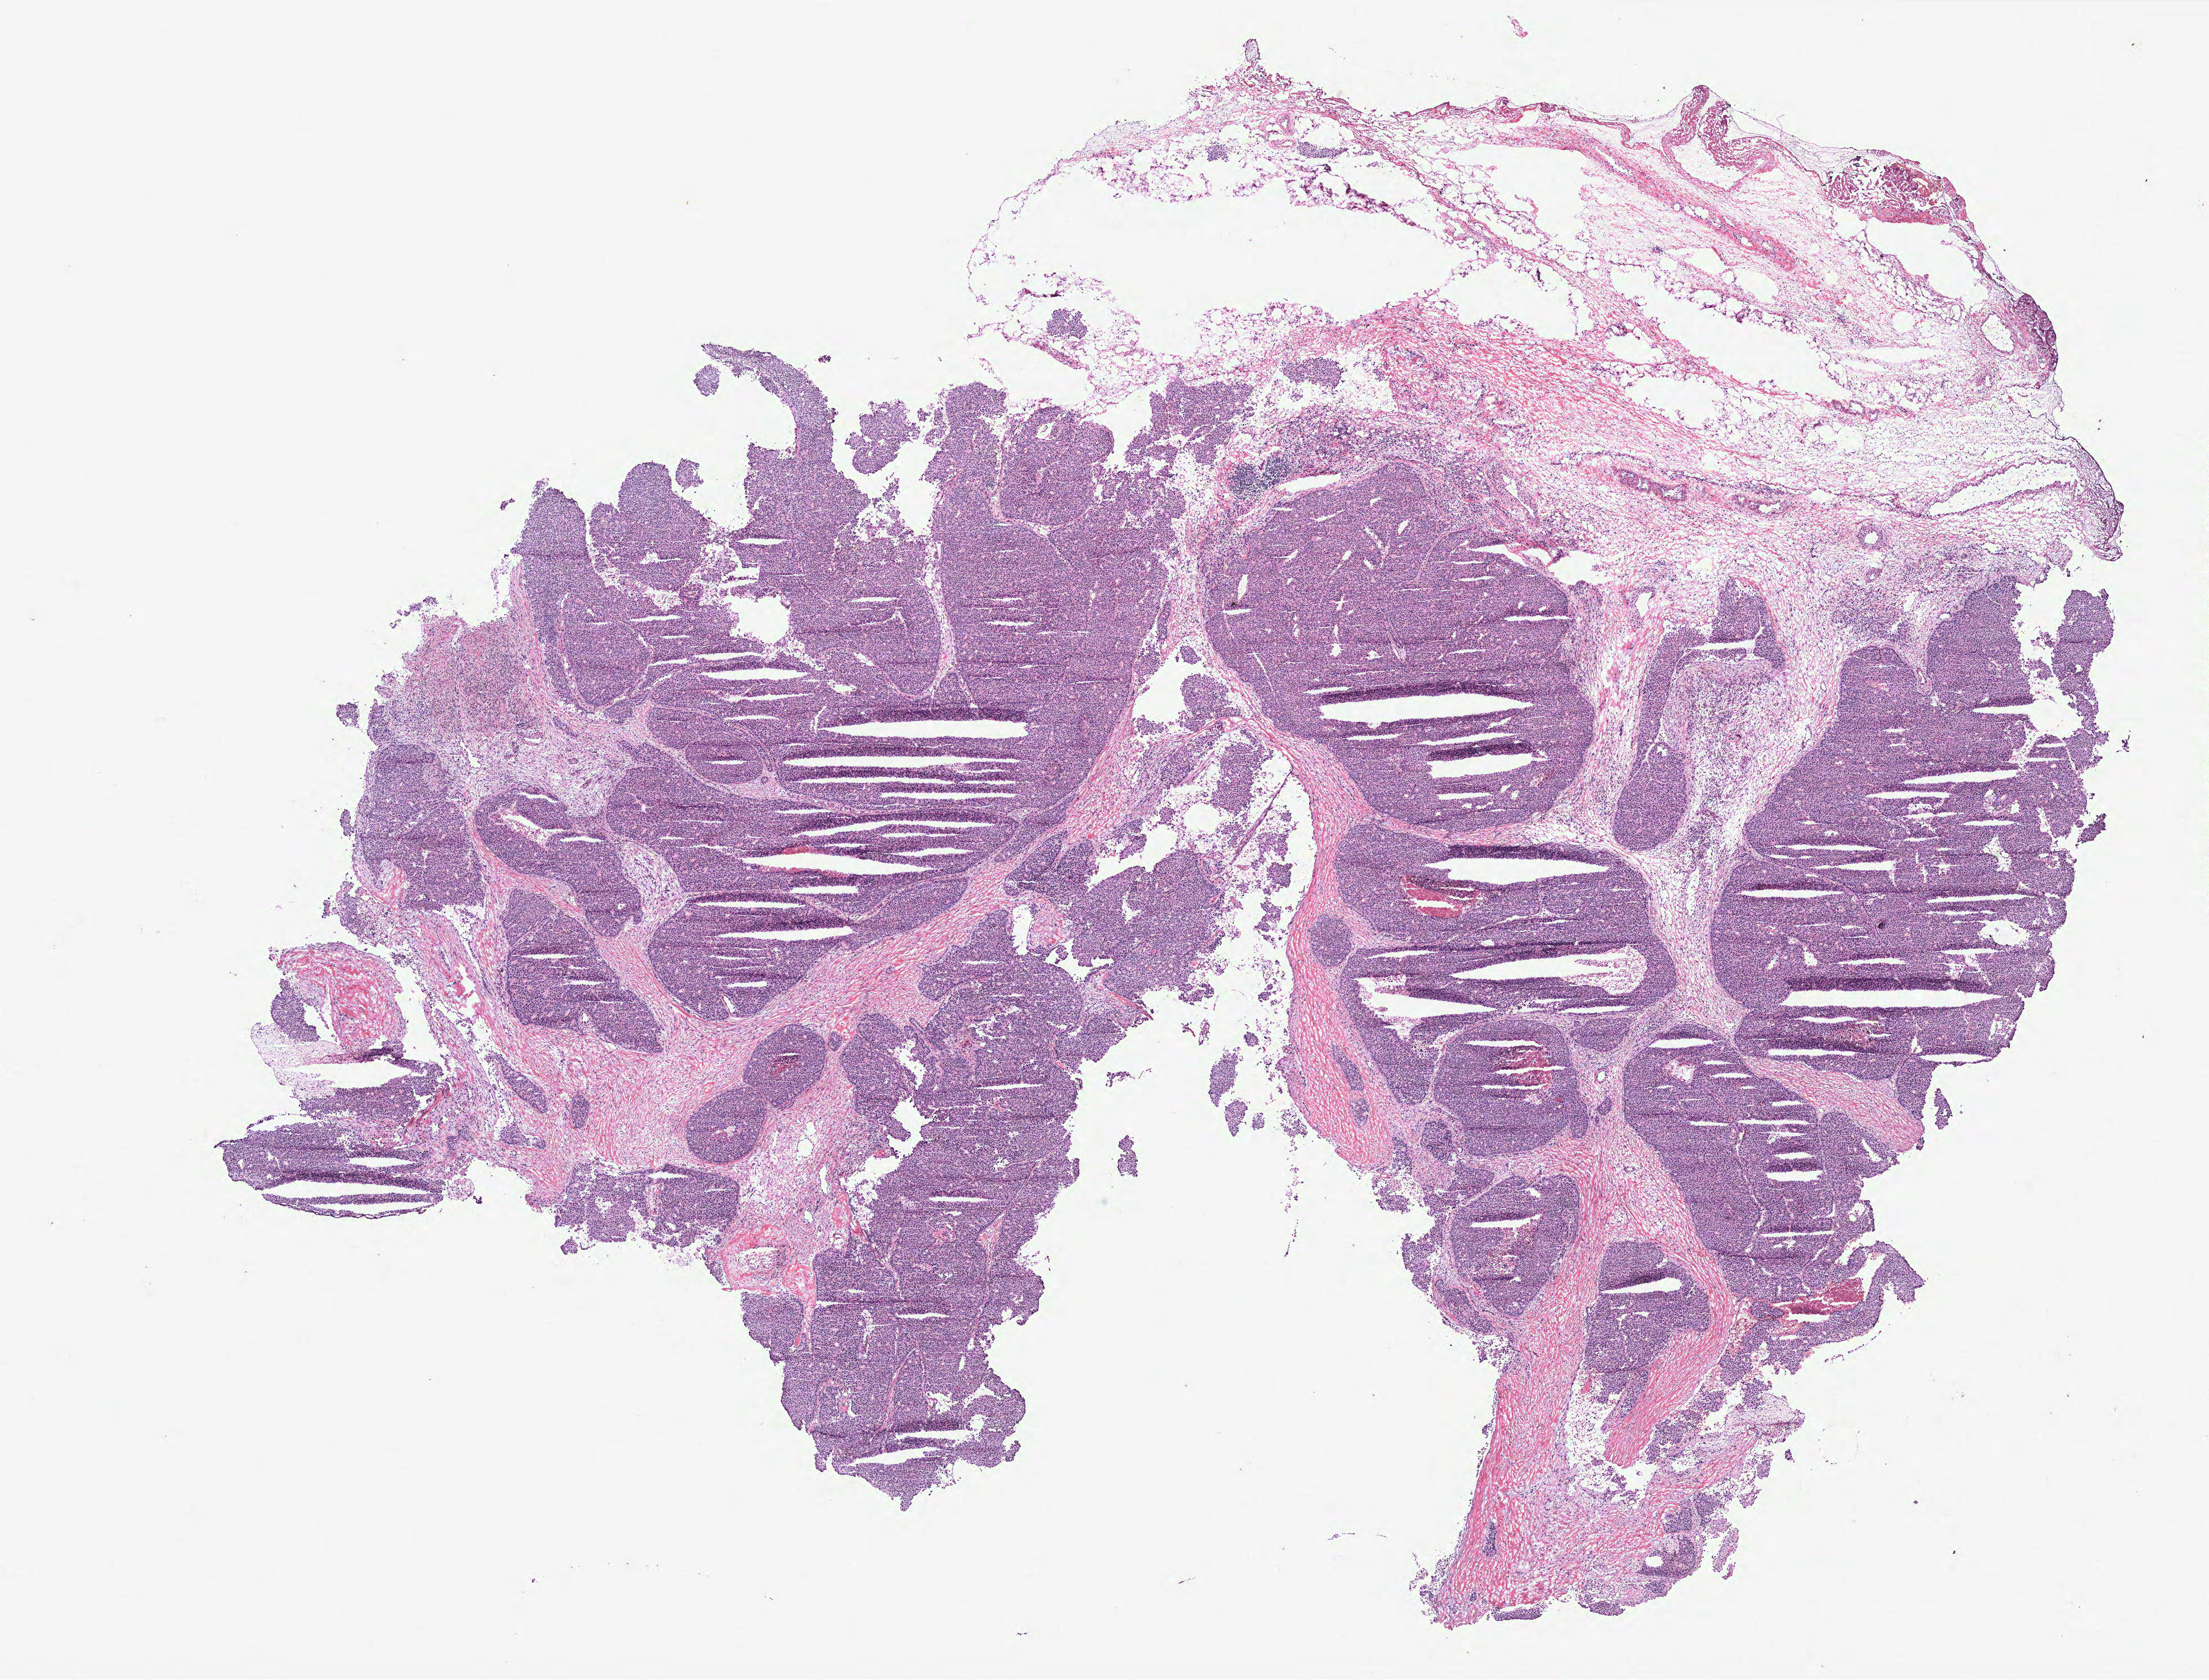
Digitized Hematoxylin and eosin (H&E) stained tissue section (whole slide) — shown as a low-resolution overview of the whole scanned area (about 15.8 x 12.1 mm, slide scanned at 40x), breast, tumour tissue. Patient: female, age 46 years.
- AJCC pathologic stage: IIIB
- histologic diagnosis: Infiltrating duct carcinoma, NOS